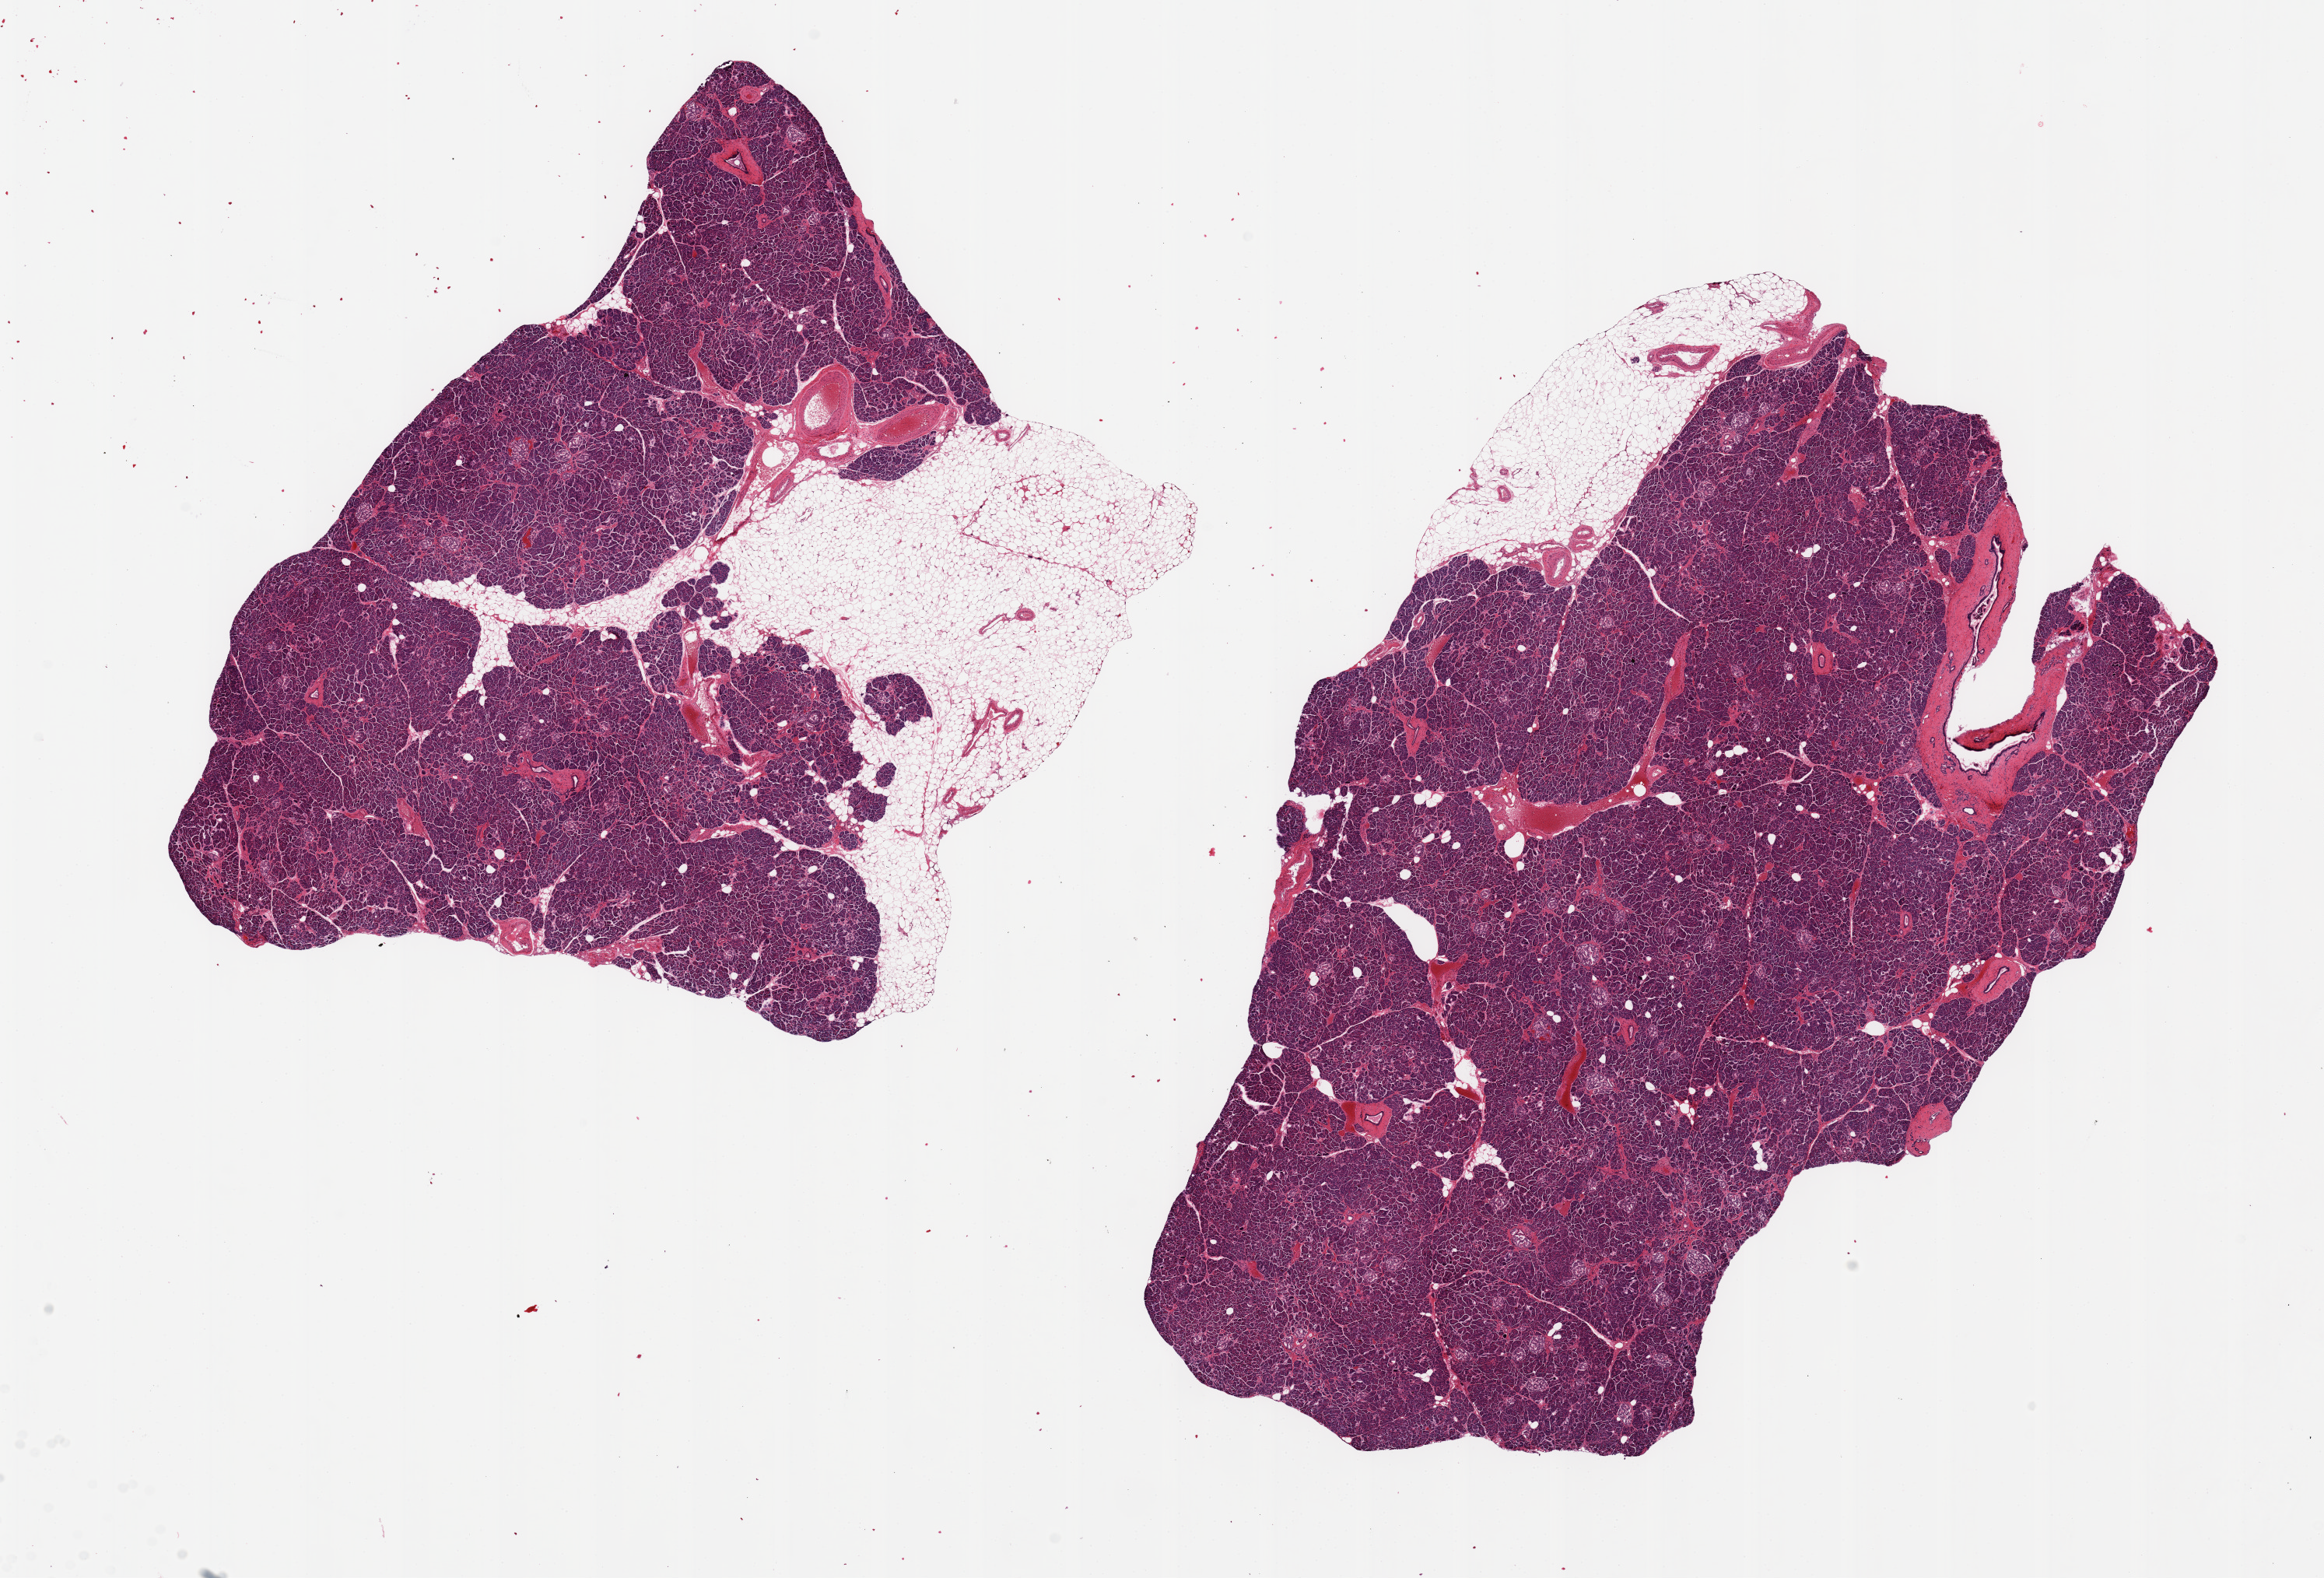
Hematoxylin and eosin (H&E) whole-slide image — whole scanned area (about 23.6 x 16.0 mm) shown as a low-resolution overview; PAXgene-fixed paraffin-embedded (PFPE) section; section of pancreas (target tissue); donor tissue sample. Male donor.
Pathologist's review note for this sample: 2 pieces ~11x8mm; Well preserved, & visible Islets; !0-20% peripheral fat.